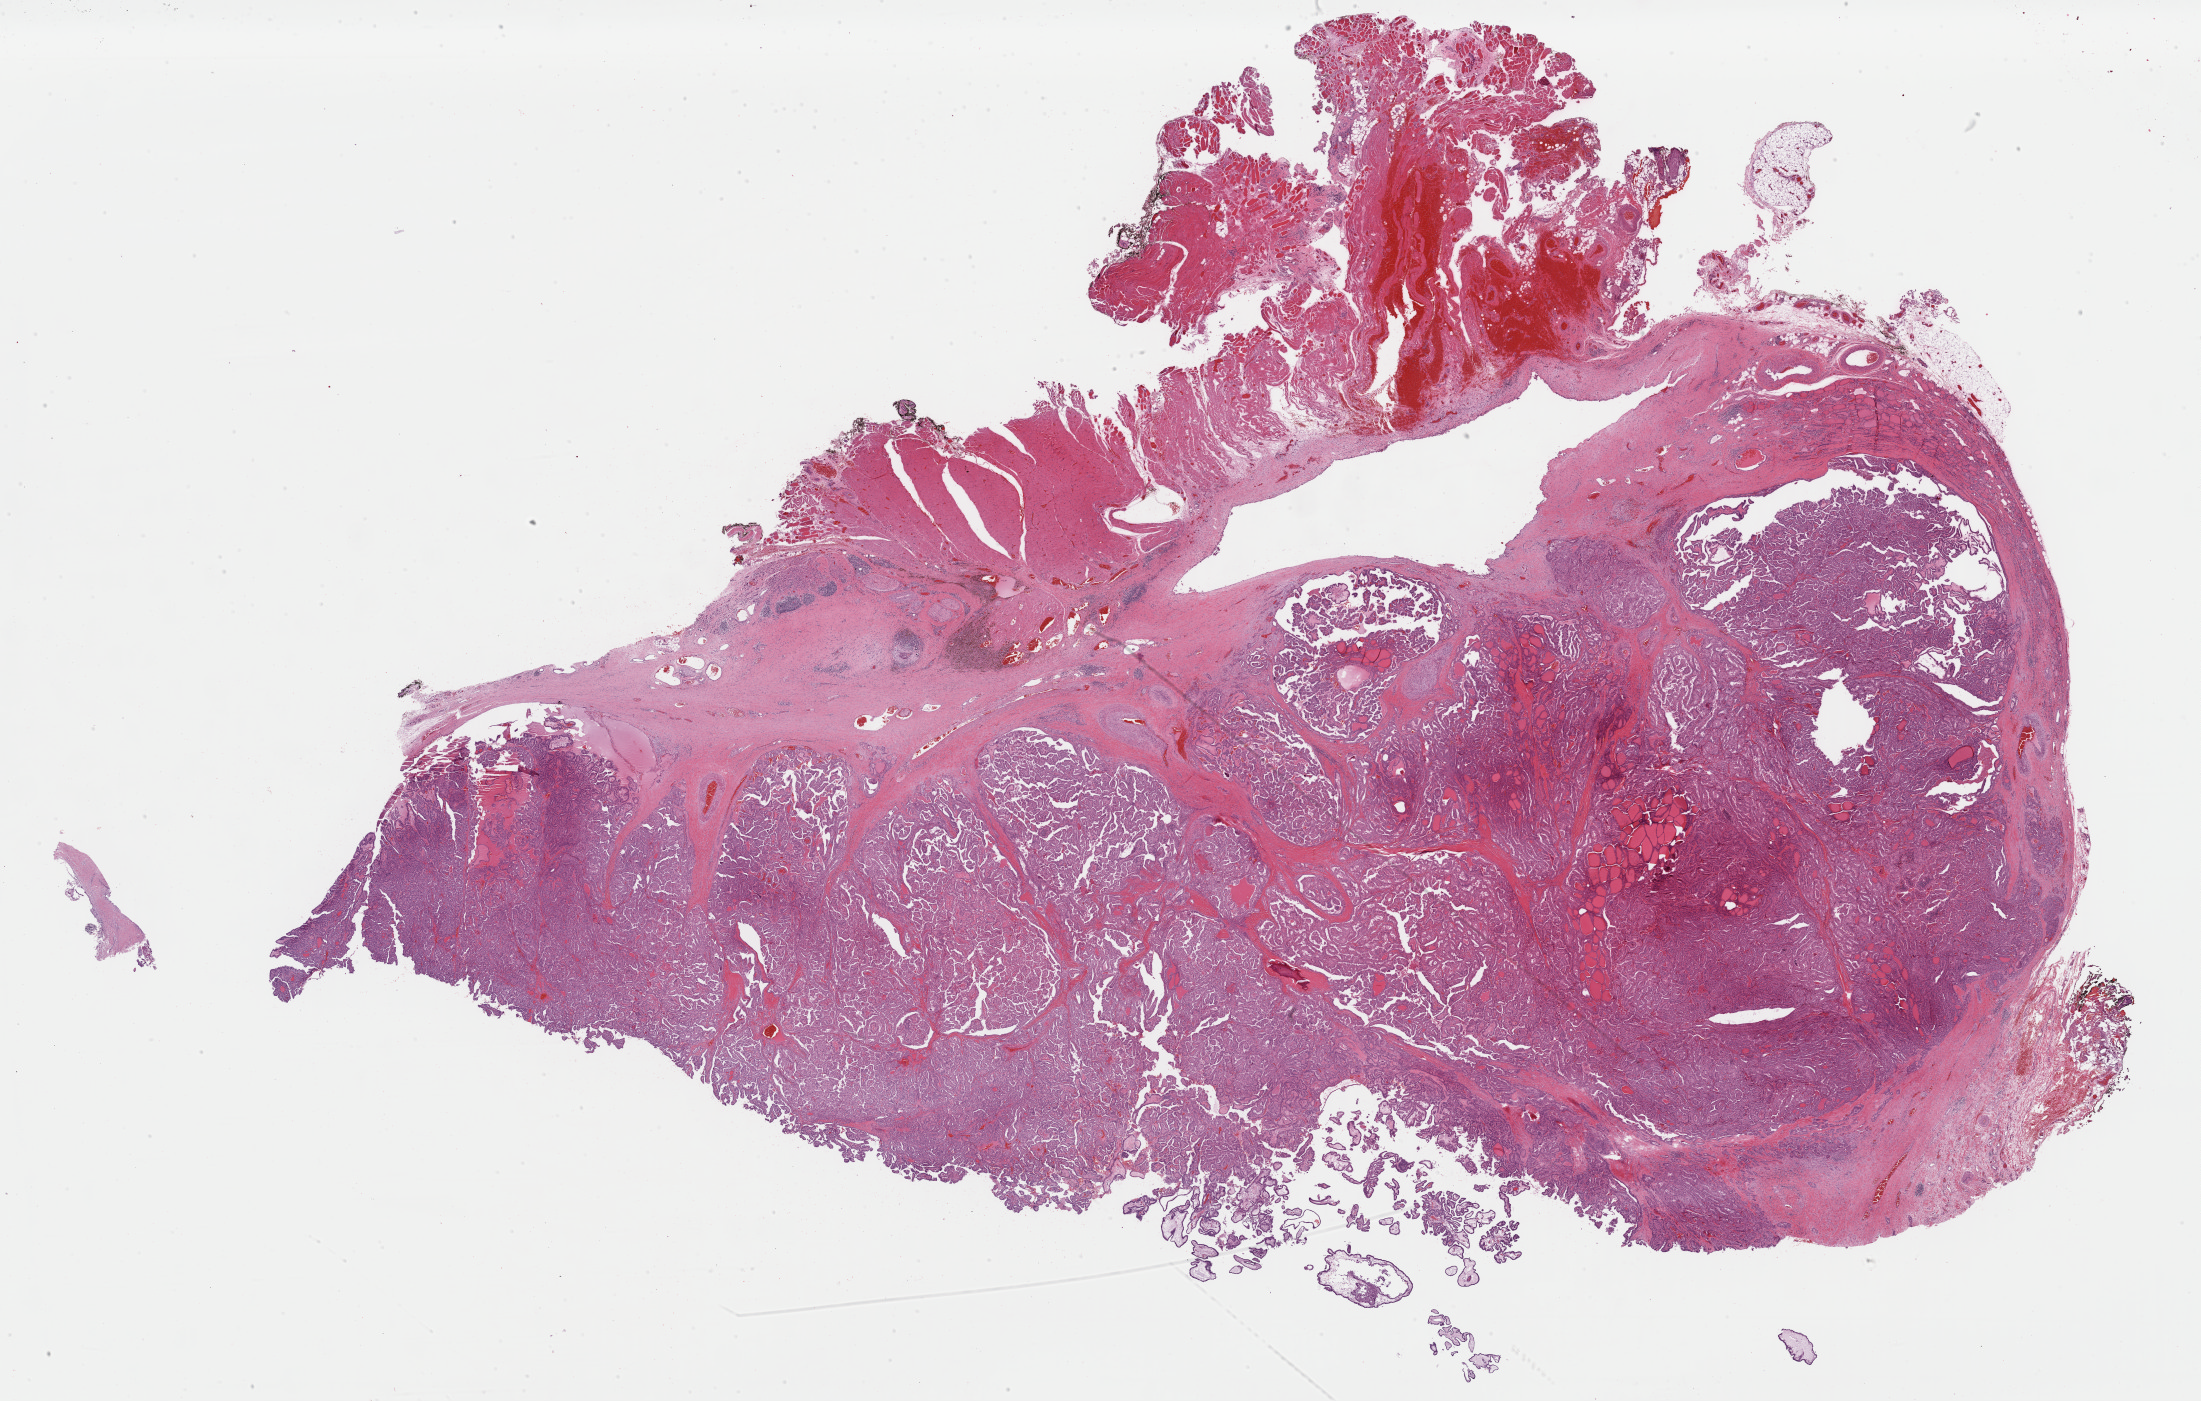
Hematoxylin and eosin (H&E) stained whole-slide image, a low-resolution overview of the entire scanned area, about 34.8 x 22.1 mm (acquisition: 40x scan); FFPE section; thyroid, primary tumour sample. Patient: female, age at initial diagnosis 42 years.
Lymph nodes positive (case pathology): 4 of 18 examined. AJCC pathologic stage: I. Histologic diagnosis: Nonencapsulated sclerosing carcinoma (thyroid gland).